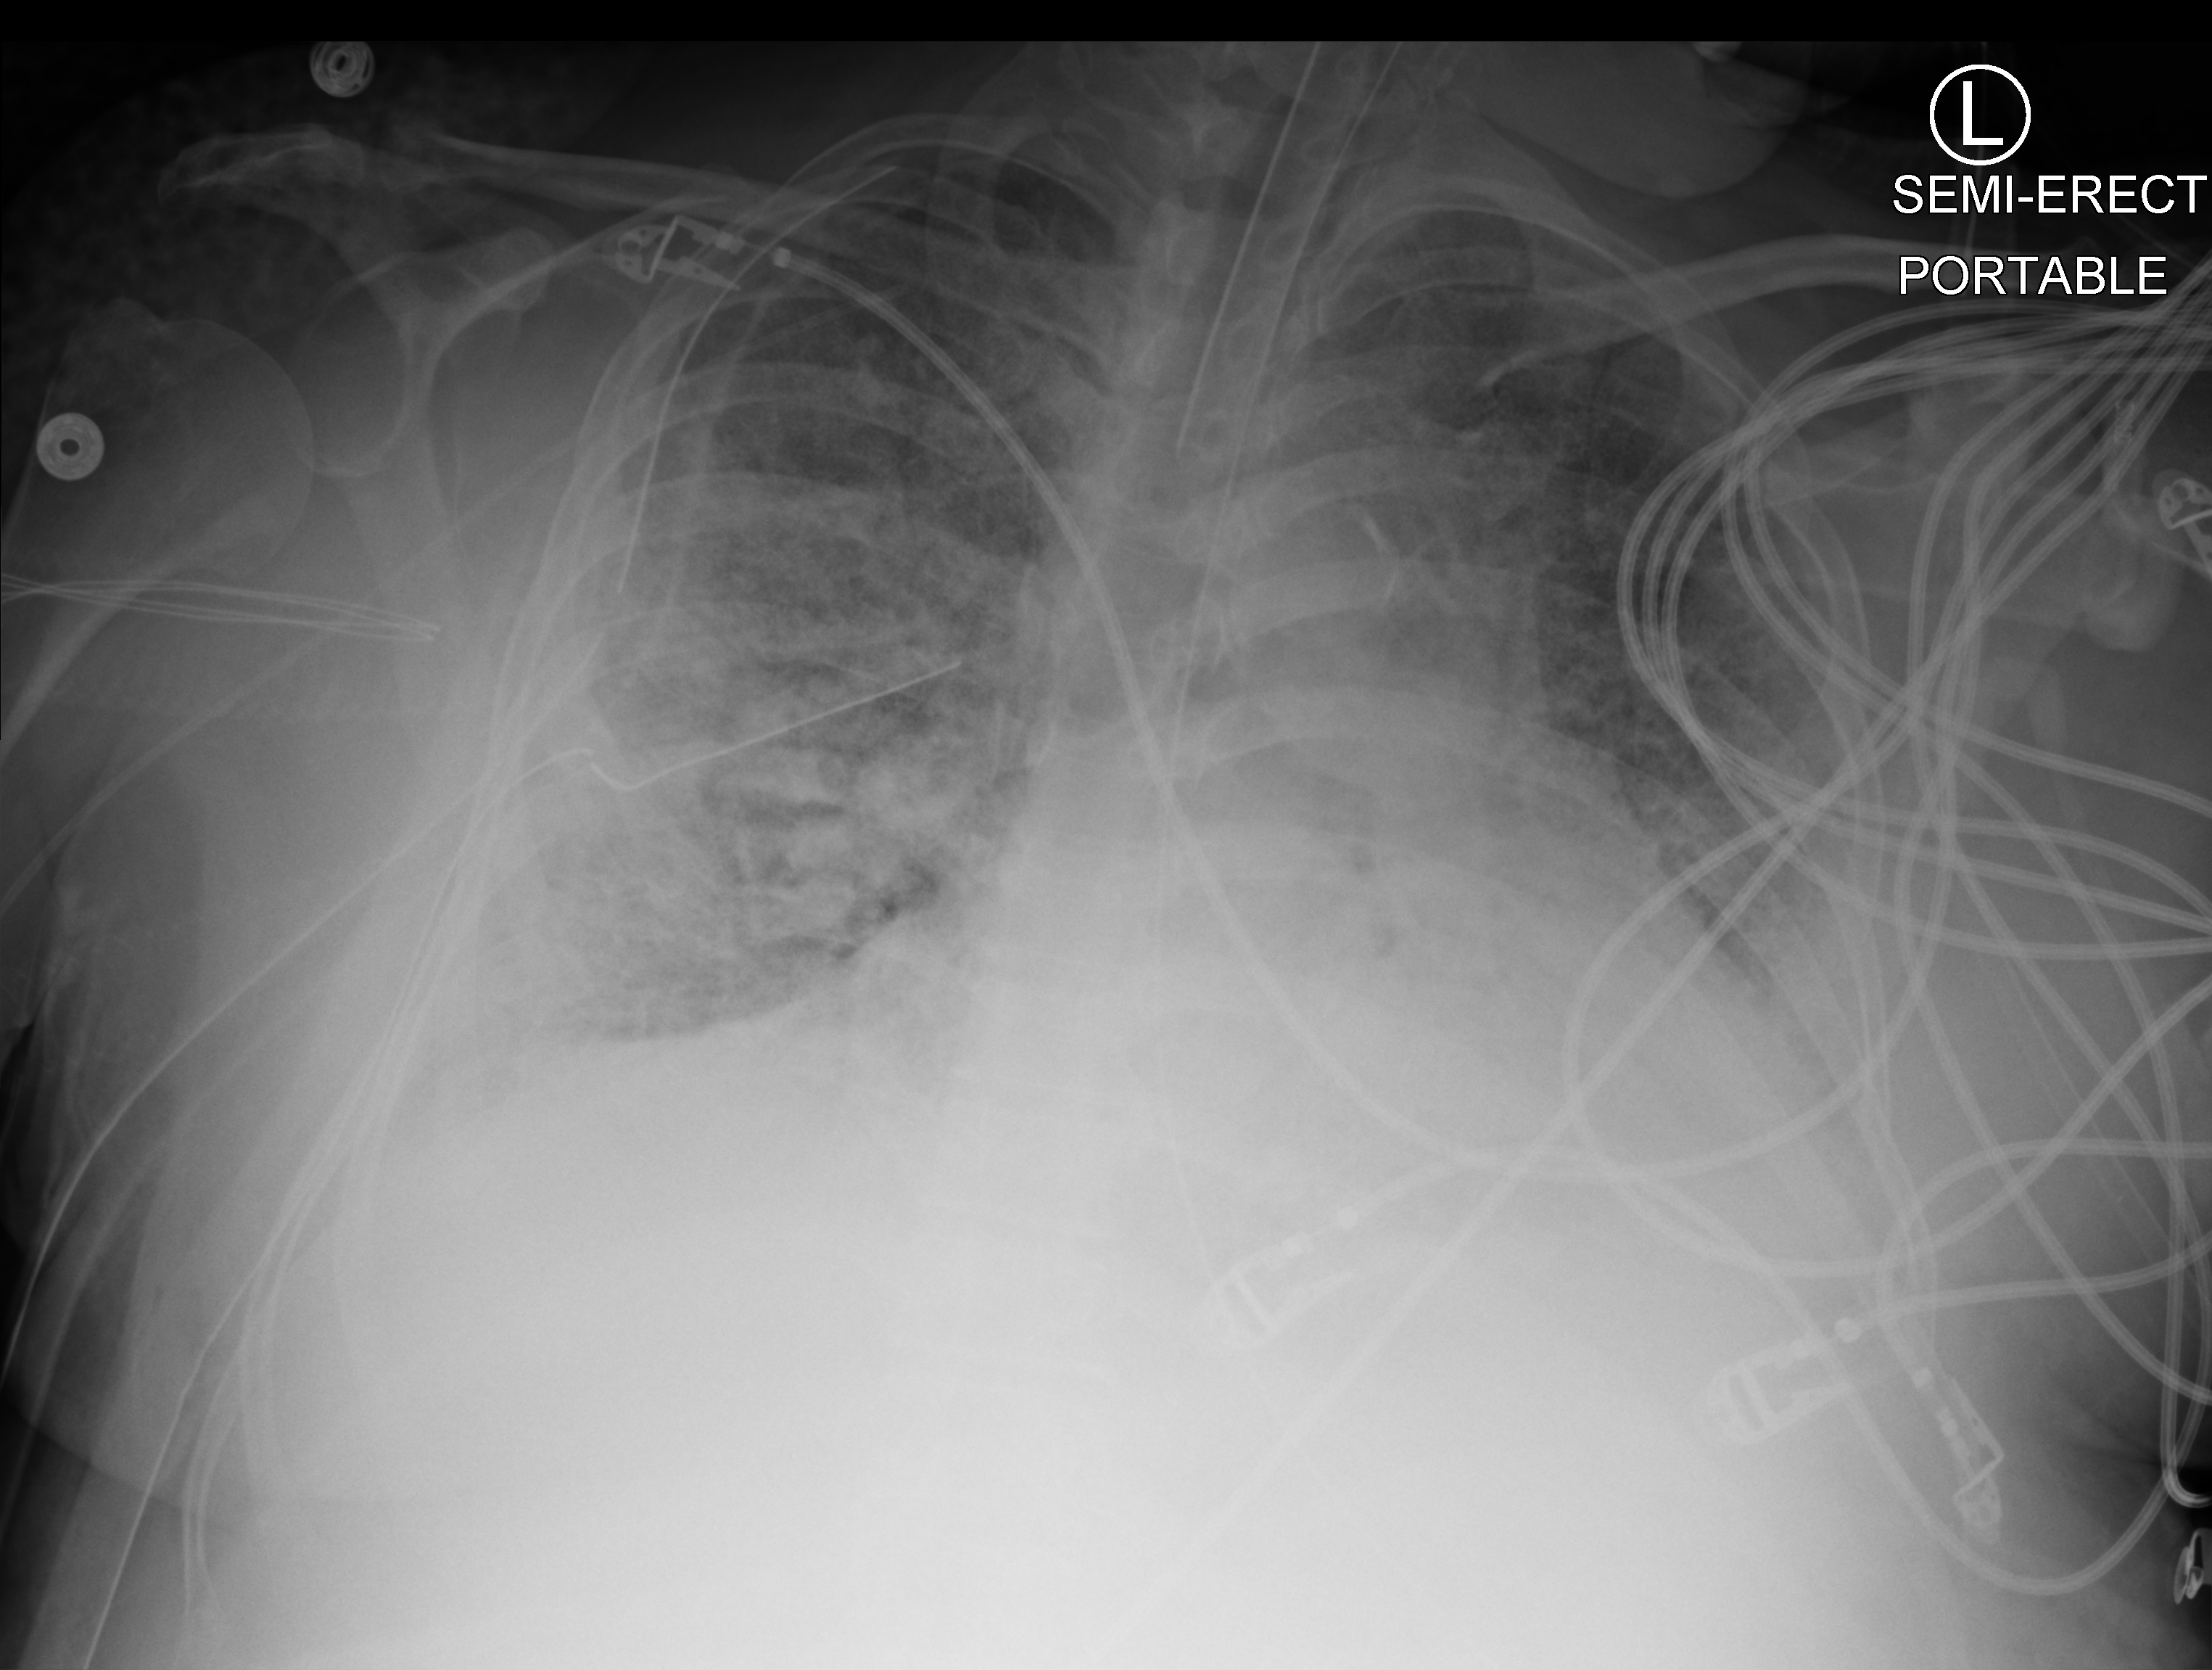
Chest X-ray (portable); anteroposterior (AP) projection. Patient hospitalised with COVID-19, aged 18–59 years.
Hospital-stay facts (about this admission, not read from this image; timing relative to this image not recorded): mechanically ventilated during this hospital stay: yes; length of hospital stay: 48 days; admitted to intensive care during this hospital stay: yes.